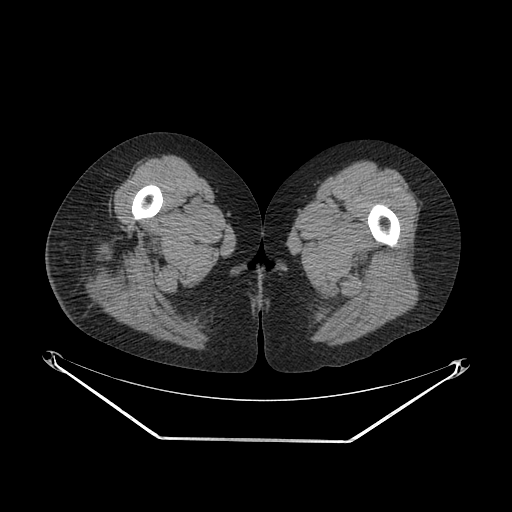
CT of an extremity soft-tissue mass (from a PET/CT study), one axial slice; position 24 of 267 along the scan axis; 140 kVp; soft-tissue window (W 400 / L 40 HU); 3.75 mm slice thickness; 512 × 512 image matrix, field of view 500 × 500 mm. Female patient. From the clinical record (not read from this slice): histological type: epithelioid sarcoma with vascular differentiation; site of the primary tumour: right buttock.
Annotated regions visible in this slice (expert contour drawn on MRI and transferred to this co-registered scan by the dataset authors):
- gross tumour volume (mass): bounding box (x1, y1, x2, y2) in pixels: (105, 258, 111, 261)